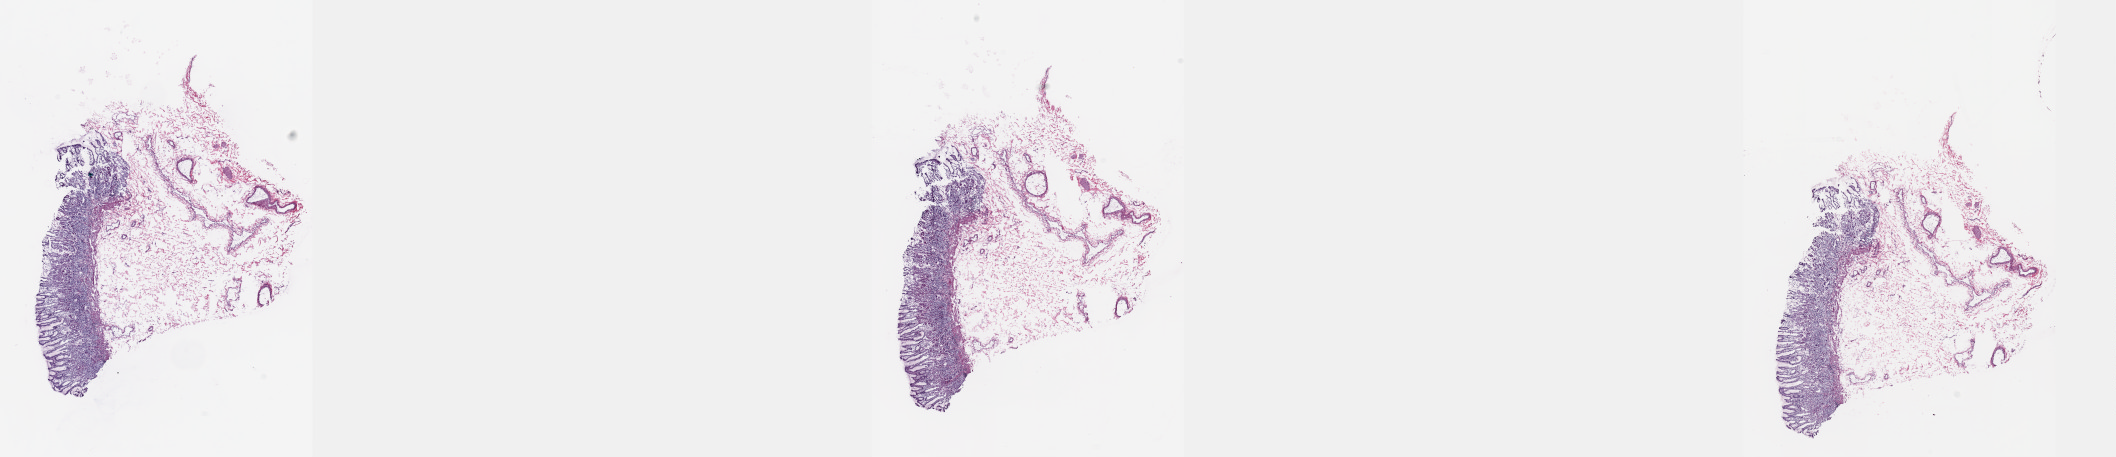
Hematoxylin and eosin (H&E) stained whole-slide image, a low-resolution overview of the entire scanned area, about 34.1 x 7.4 mm. Frozen section. Esophagus, solid tissue normal (non-tumour tissue) sample. Patient: male, age at initial diagnosis 67 years. Slide review estimates, as recorded: tumour cells 0%, tumour nuclei 0%, normal cells 100%, stromal cells 0%, necrosis 0%. Infiltration values recorded for this section: lymphocyte infiltration 3%, monocyte infiltration 0%, neutrophil infiltration 0%.
This section: solid tissue normal sample (biorepository sample class). Patient diagnosis: Squamous cell carcinoma, NOS (lower third of esophagus).